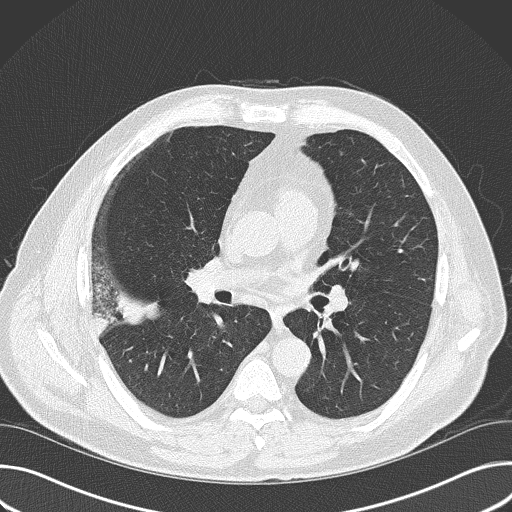
Axial slice from a low-dose chest CT screening exam; first (baseline) screen; lung window (W 1500 / L -600 HU); 2 mm slice thickness; slice 90 of 157 in the series; 512 × 512 image matrix, field of view 380 × 380 mm. Male participant, aged 56 years at enrolment. Current smoker at enrolment.
• Expert-annotated lung lesion, box from (x=78, y=253) to (x=182, y=355) px.
• The exam's reader record, not a measurement of the box and not confirmed to be the same lesion: non-calcified nodule or mass ≥4 mm, right upper lobe, 6 × 5 mm, spiculated (stellate) margins, soft tissue attenuation.
• Official screen result: positive, change unspecified: nodule(s) >= 4 mm or enlarging nodule(s), mass(es), or other non-specific abnormalities suspicious for lung cancer.
• Later outcome: lung cancer diagnosed 16 days after this screen — adenocarcinoma, NOS, right upper lobe, poorly differentiated (G3), stage IIB (AJCC 6th edition), 60 mm at pathology.